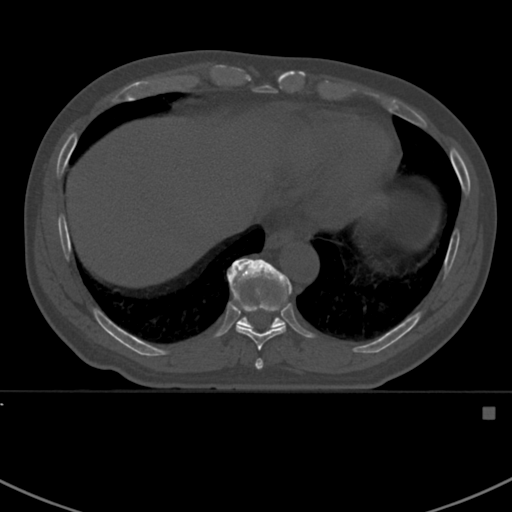
CT including the spine, one axial slice; slice 378 of 412 in the series (ordered by position); 120 kVp; bone window (W 1800 / L 400 HU); 1.5 mm slice thickness; 512 × 512 image matrix, field of view 358 × 358 mm. Patient: male, 59 years. From the clinical record (not read from this slice): primary cancer: prostate.
Annotated regions visible in this slice (semi-automatically segmented with operator editing):
- T10 vertebra: box from (x=227, y=258) to (x=292, y=328) px
- T8 vertebra: (x=255, y=359)–(x=263, y=370)
- T9 vertebra: (x=227, y=304)–(x=286, y=351)